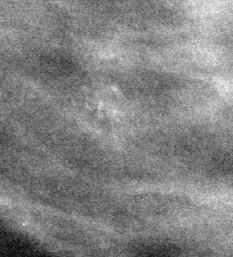
Region of interest cut from a scanned film mammogram (one marked finding); left breast; MLO view.
Marked abnormality: calcifications, morphology pleomorphic, distribution clustered; BI-RADS assessment category 4; subtlety rating 3 on a 1 (subtle) to 5 (obvious) scale; pathology result (as recorded, not read from the image): benign.